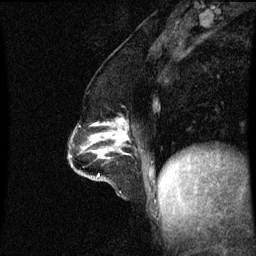
Breast MRI (dynamic contrast-enhanced), one sagittal slice. Slice 26 of 60 in the series (ordered by position). Dynamic contrast-enhanced series, image 2 of 3 at this slice position (ordered by acquisition). 1.5 T. TE 4.2 ms, TR 8.9 ms. 256 × 256 image matrix, field of view 200 × 200 mm. Female patient, age 47 years. From the clinical record (not read from this slice): setting: breast cancer imaged before/during neoadjuvant chemotherapy; receptor status: HR-positive, HER2-negative.
Structures marked on this image (semi-automatic segmentation, software-assisted and operator-edited):
- analysis volume of interest (the breast-tissue region the enhancement analysis was run in; not a lesion): bounding box (x1, y1, x2, y2) in pixels: (71, 120, 130, 163)
- tumour enhancement mask (voxels above the 70 % enhancement threshold inside the analysis volume of interest): (96, 122, 128, 143)